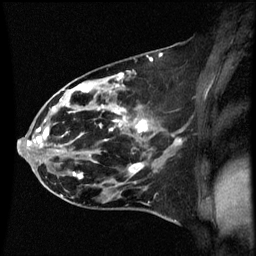
Breast MRI (dynamic contrast-enhanced), one sagittal slice. Position 29 of 60 along the scan axis. Dynamic contrast-enhanced series, image 2 of 3 at this slice position (ordered by acquisition). 1.5 T. TE 4.2 ms, TR 8.9 ms. 256 × 256 image matrix, field of view 200 × 200 mm. Patient: female, 44 years. From the clinical record (not read from this slice): setting: breast cancer imaged before/during neoadjuvant chemotherapy; receptor status: HR-positive, HER2-negative.
Annotated regions visible in this slice (semi-automatic segmentation, software-assisted and operator-edited):
- analysis volume of interest (the breast-tissue region the enhancement analysis was run in; not a lesion): bounding box [x1, y1, x2, y2] px = [43, 78, 153, 189]
- tumour enhancement mask (voxels above the 70 % enhancement threshold inside the analysis volume of interest): [61, 78, 148, 177]